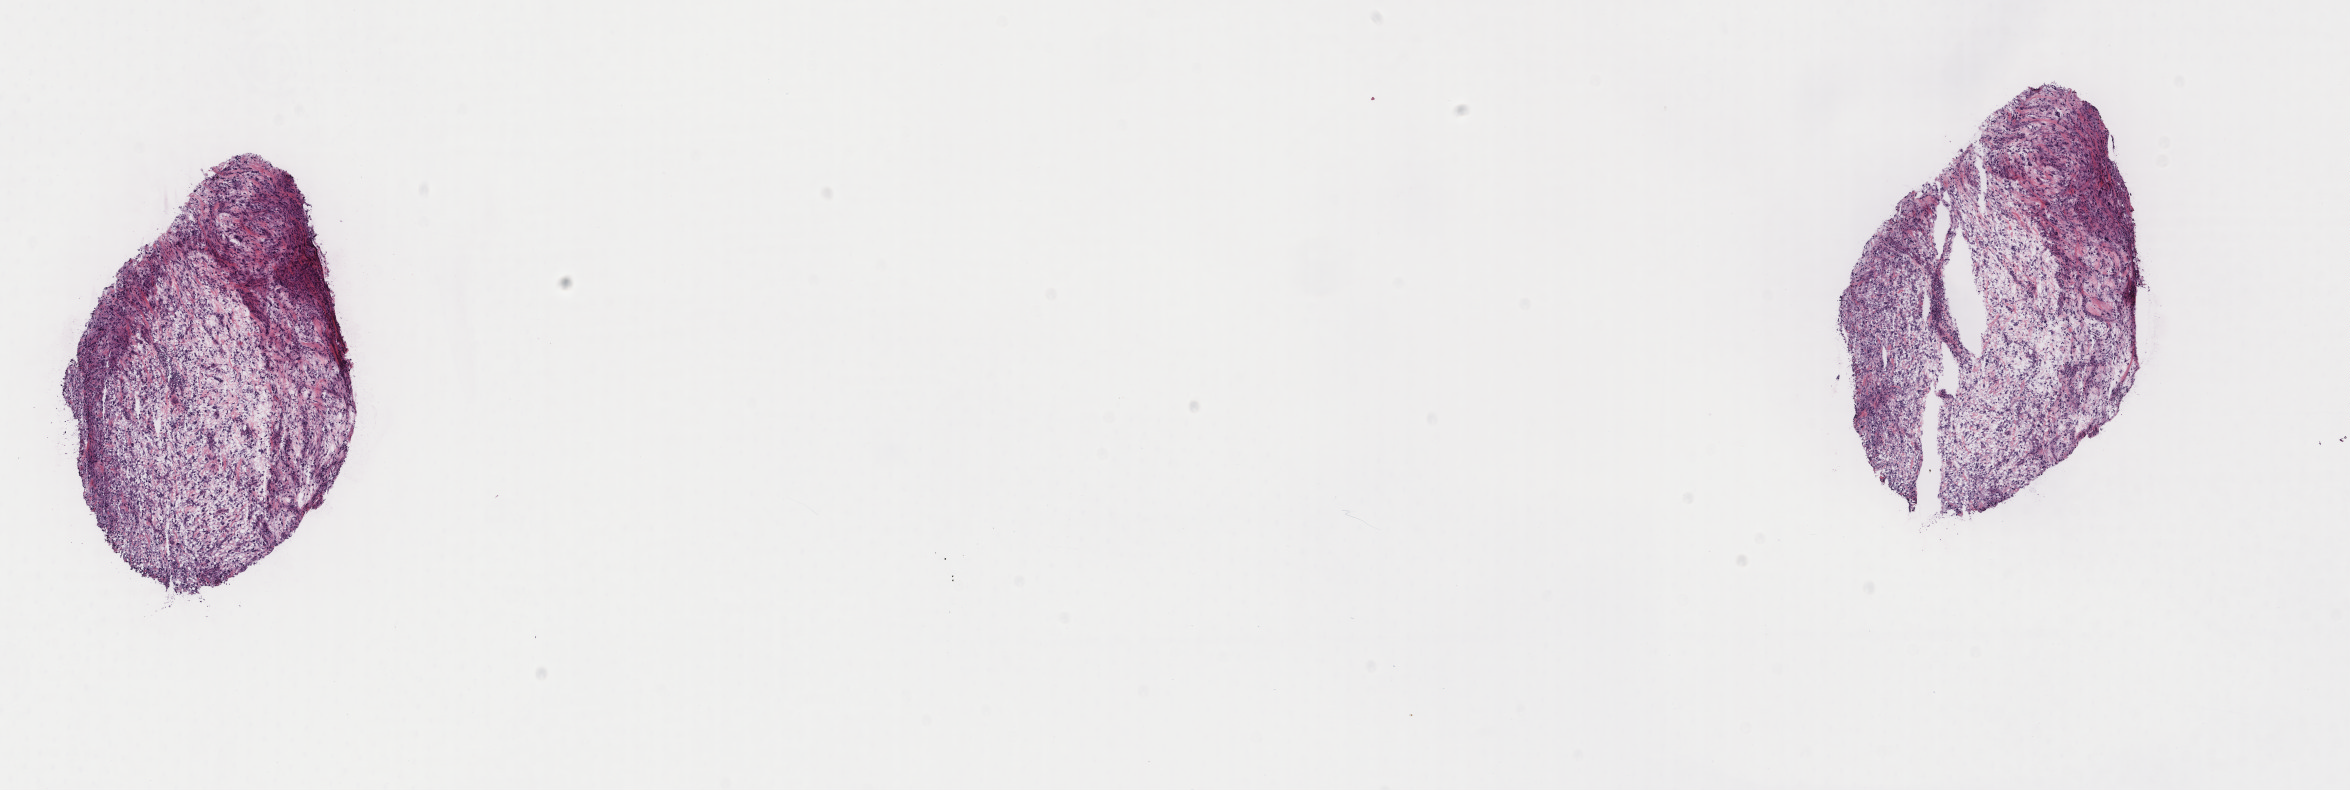
Whole-slide histology image, H&E, shown as a low-resolution overview of the whole scanned area (about 18.7 x 6.3 mm), frozen section, sample: primary tumour, connective, subcutaneous and other soft tissues. Female, age 84 years at initial diagnosis. Composition of this section per pathologist review: tumour cells 100%, tumour nuclei 90%, normal cells 0%, stromal cells 0%, necrosis 0%. Inflammatory infiltration, as recorded: lymphocyte infiltration 0%, monocyte infiltration 0%, neutrophil infiltration 0%.
Histologic diagnosis: Giant cell sarcoma.